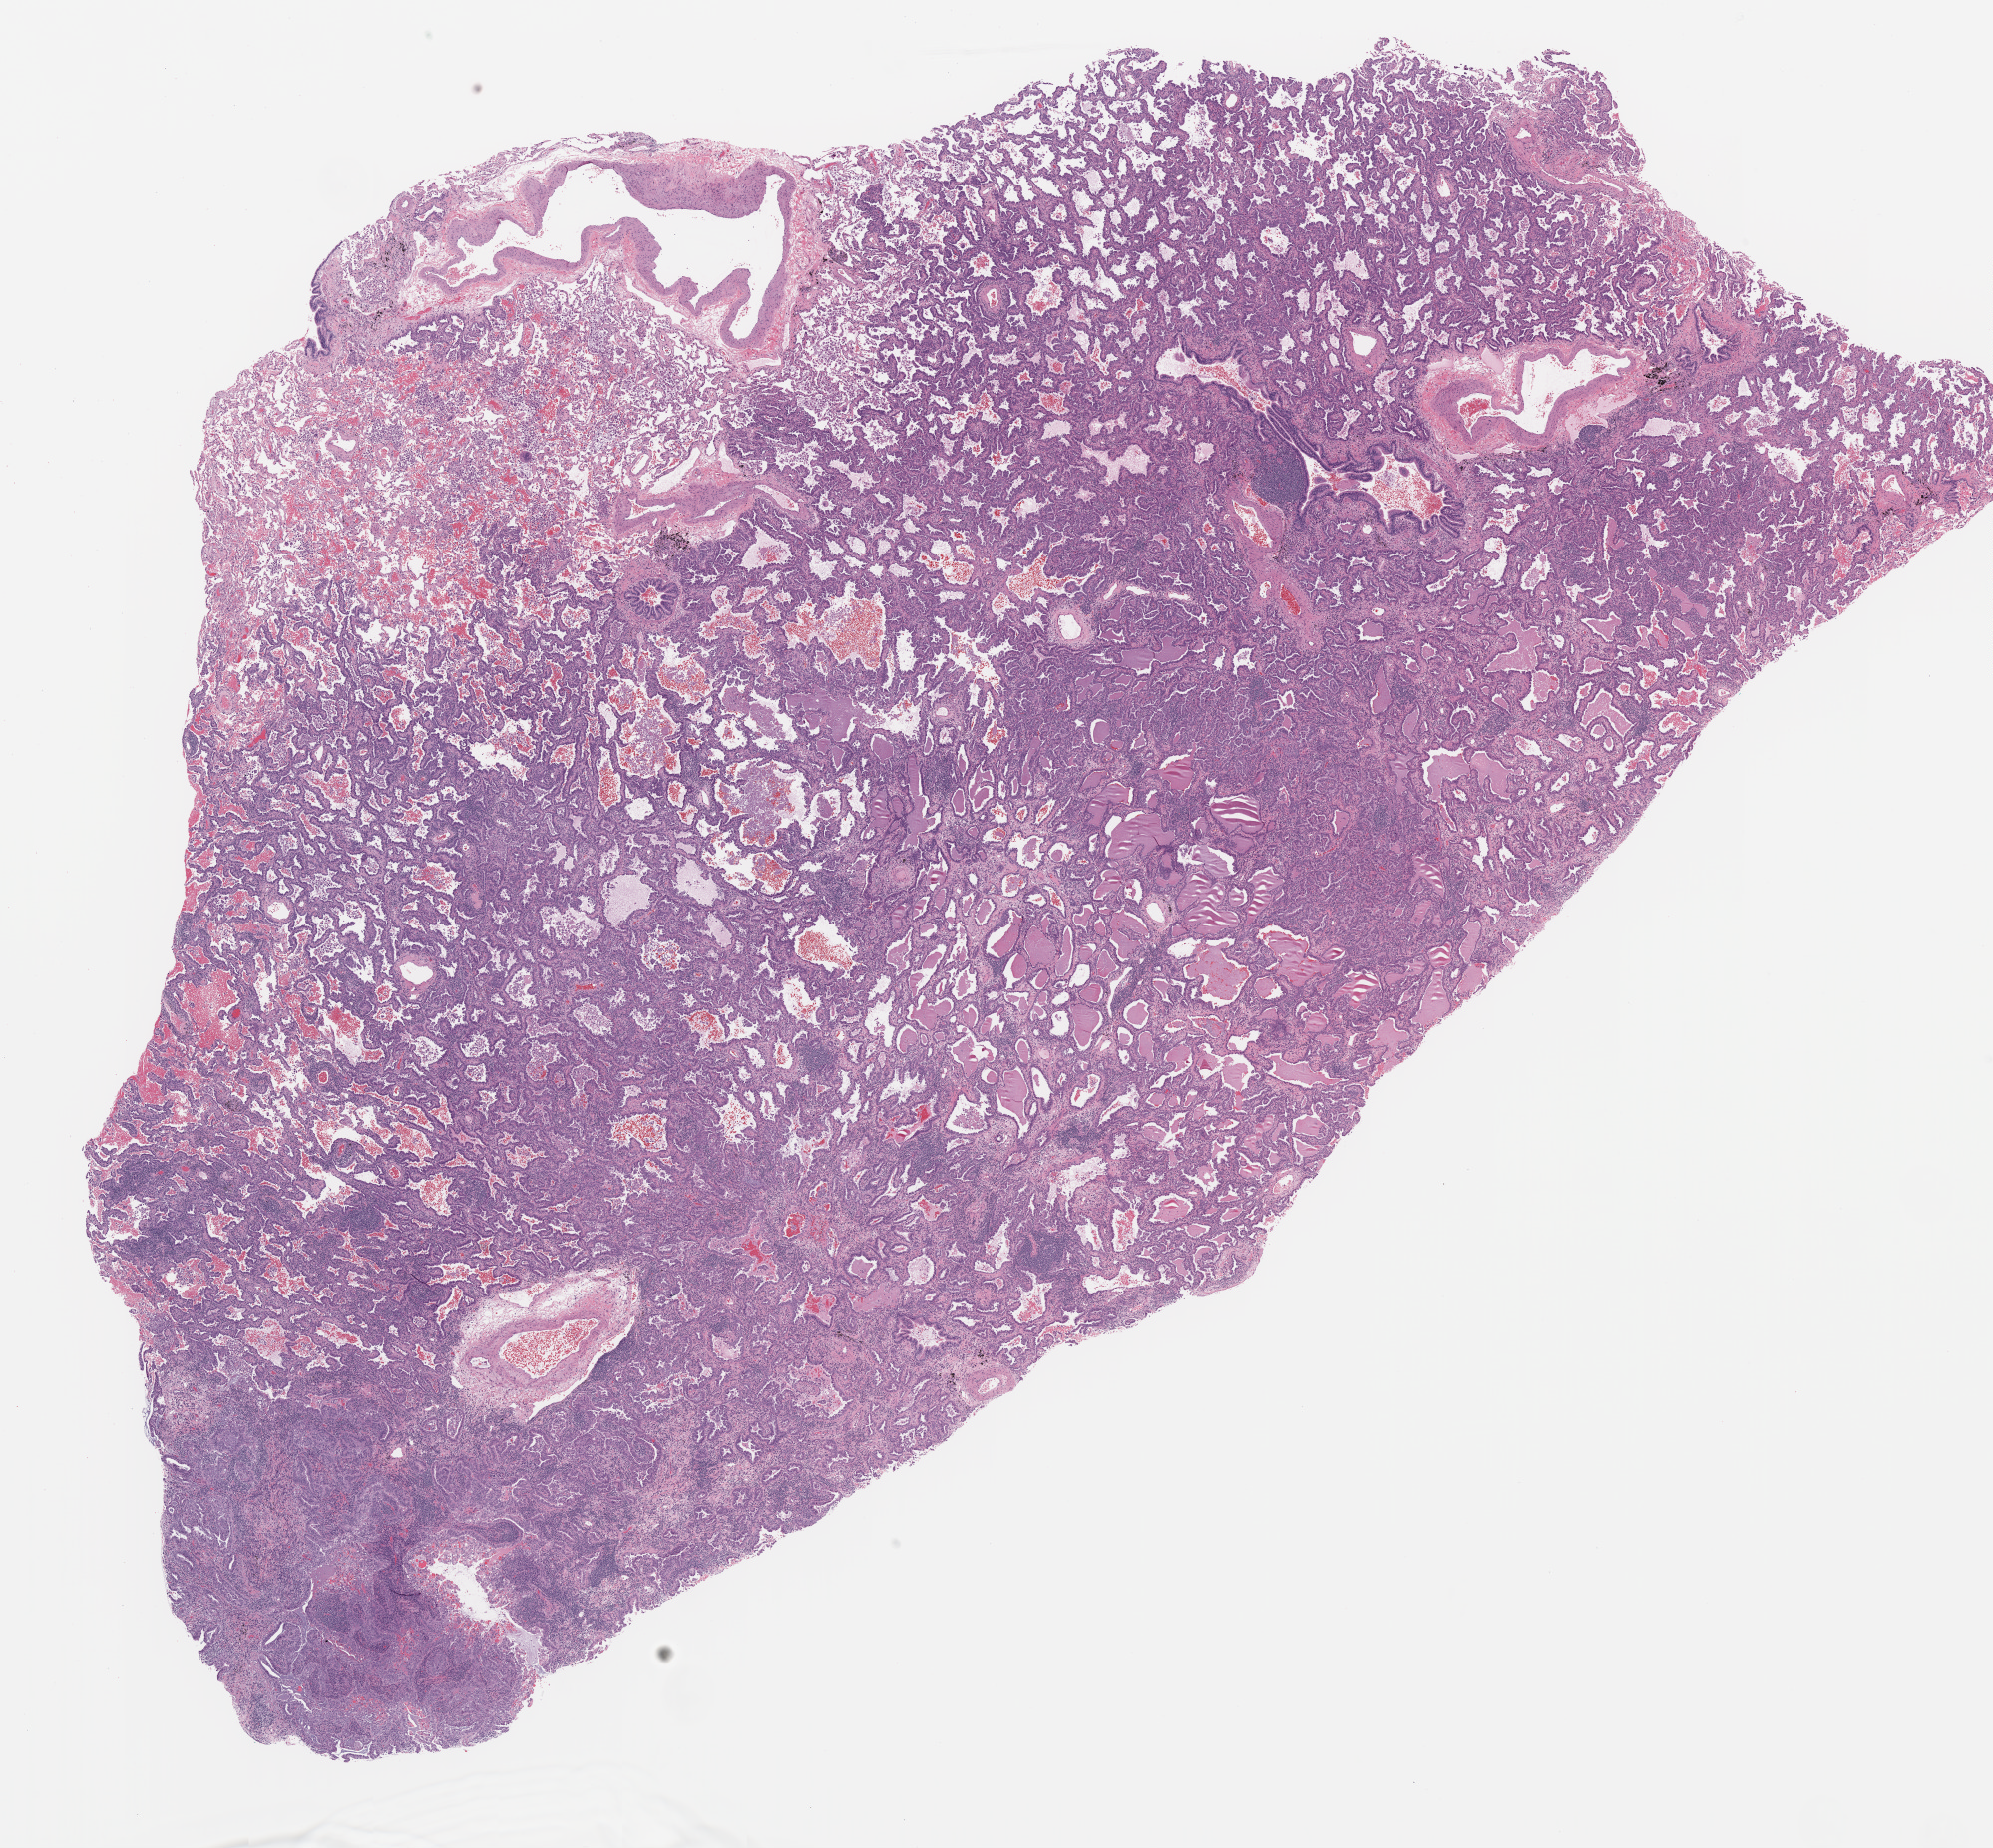
Whole-slide histology image, H&E-stained, low-resolution overview of the scanned area, about 16.0 x 14.8 mm; formalin-fixed paraffin-embedded (FFPE) diagnostic section; primary tumour sample from the lung. Female patient.
AJCC pathologic stage: IIB. Laterality: left. Histologic diagnosis: Adenocarcinoma, NOS.